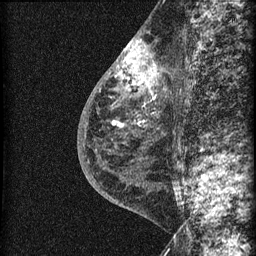
Breast MRI (dynamic contrast-enhanced), one sagittal slice. Slice 29 of 60 in the series (ordered by position). Dynamic contrast-enhanced series, image 2 of 3 at this slice position (ordered by acquisition). 1.5 T. TE 4.2 ms, TR 22.7 ms. 1.5 mm slice thickness. 256 × 256 image matrix, field of view 180 × 180 mm. Patient: female, 48 years. Case-level facts recorded for this patient, not image findings: setting: breast cancer imaged before/during neoadjuvant chemotherapy; receptor status: triple-negative.
Annotated regions visible in this slice (semi-automatically segmented with operator editing):
- analysis volume of interest (the breast-tissue region the enhancement analysis was run in; not a lesion): bounding box [x1, y1, x2, y2] px = [115, 34, 169, 162]
- tumour enhancement mask (voxels above the 90 % enhancement threshold inside the analysis volume of interest): [121, 39, 157, 91]